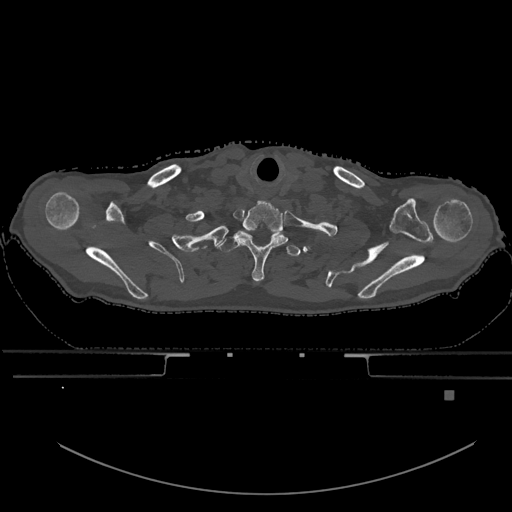
CT including the spine, one axial slice; position 562 of 969 along the scan axis; bone window (W 1800 / L 400 HU); 512 × 512 image matrix. Patient: male, 82 years. From the clinical record (not read from this slice): primary cancer: prostate; vertebrae with lytic lesions (as recorded): T11, T9, T8, T2.
Outlined on this slice (semi-automatic segmentation, software-assisted and operator-edited):
- T1 vertebra: box from (x=218, y=235) to (x=300, y=258) px